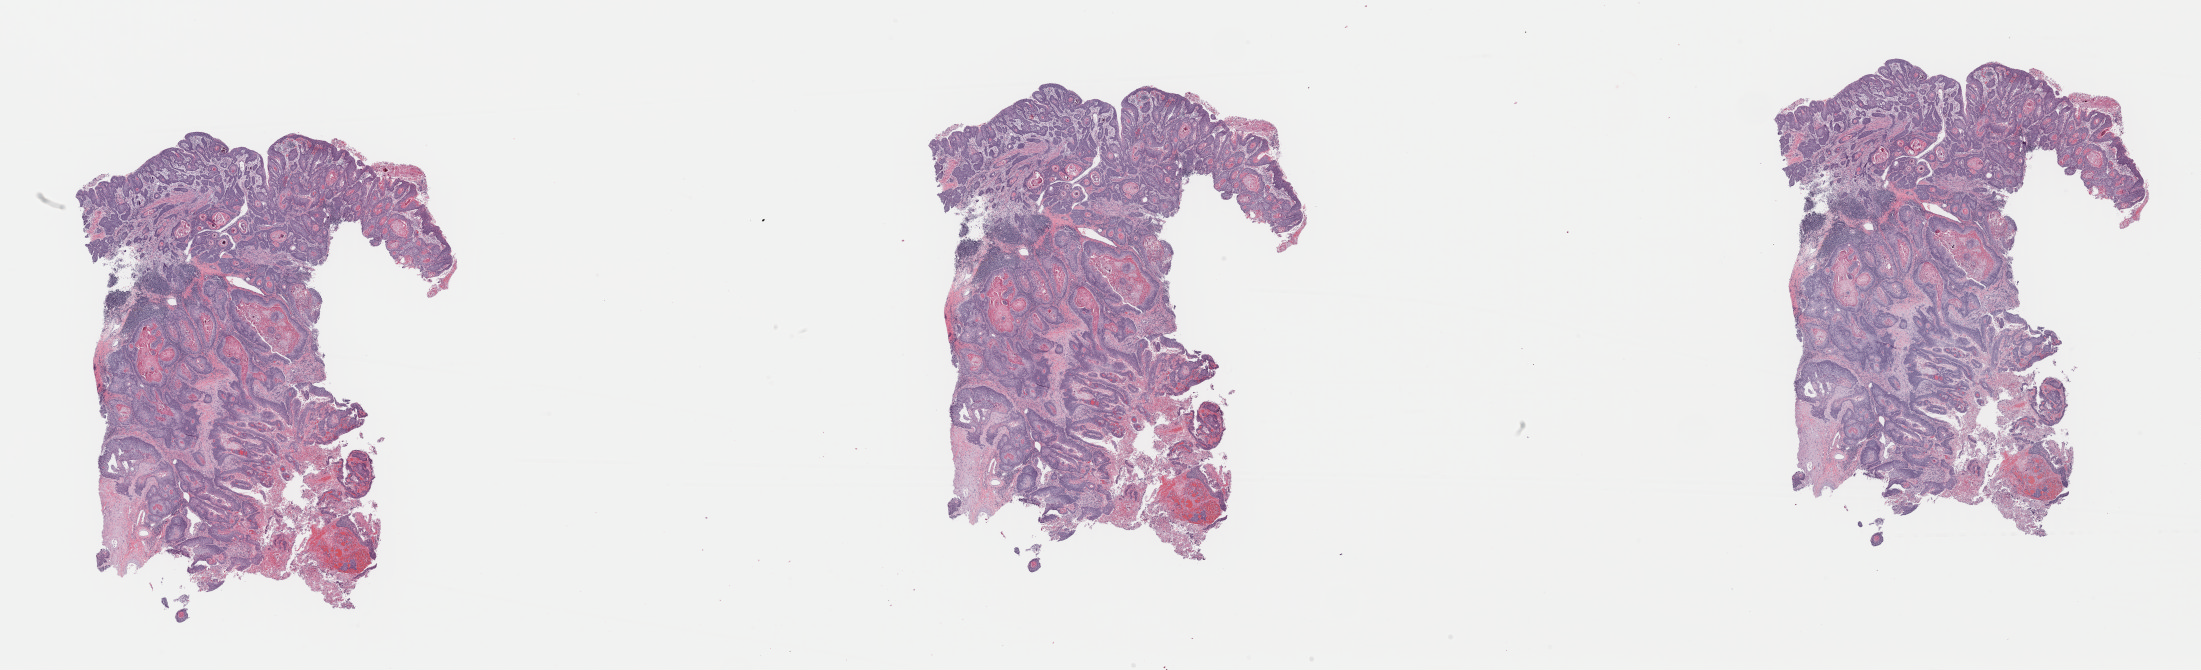
Whole-slide histology image, Hematoxylin and eosin (H&E) stained, whole scanned area (about 34.7 x 10.6 mm) shown as a low-resolution overview, formalin-fixed paraffin-embedded (FFPE) diagnostic section, head and neck, primary tumour sample. Male patient; age at initial diagnosis 47 years. Histologic grade: G2 (moderately differentiated).
• AJCC pathologic stage: IVA (7th edition)
• diagnosis: Squamous cell carcinoma, keratinizing, NOS (larynx, NOS)